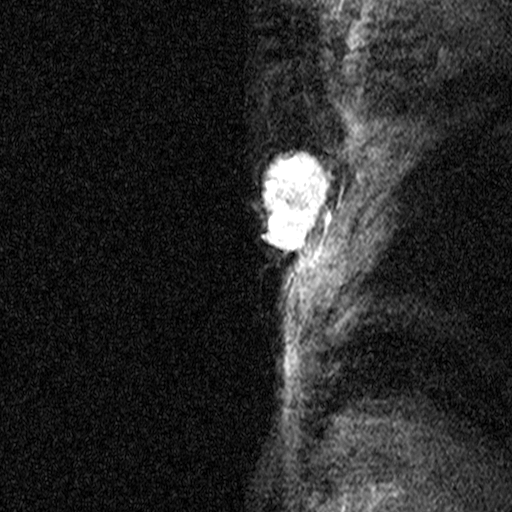
Breast MRI (dynamic contrast-enhanced), one sagittal slice. Position 36 of 44 along the scan axis. Dynamic contrast-enhanced study with each time point stored as its own series, time point 2 of 3 at this slice position (early post-contrast, ordered by acquisition time). 1.5 T. TE 4.5 ms, TR 11 ms. 512 × 512 image matrix. Patient: female, 44 years. From the clinical record (not read from this slice): setting: breast cancer imaged before/during neoadjuvant chemotherapy; receptor status: HR-positive, HER2-negative.
Outlined on this slice (semi-automatic segmentation, software-assisted and operator-edited):
- analysis volume of interest (the breast-tissue region the enhancement analysis was run in; not a lesion): bounding box <218,118,341,291> (left, top, right, bottom; pixels)
- tumour enhancement mask (voxels above the 90 % enhancement threshold inside the analysis volume of interest): <254,150,335,254>